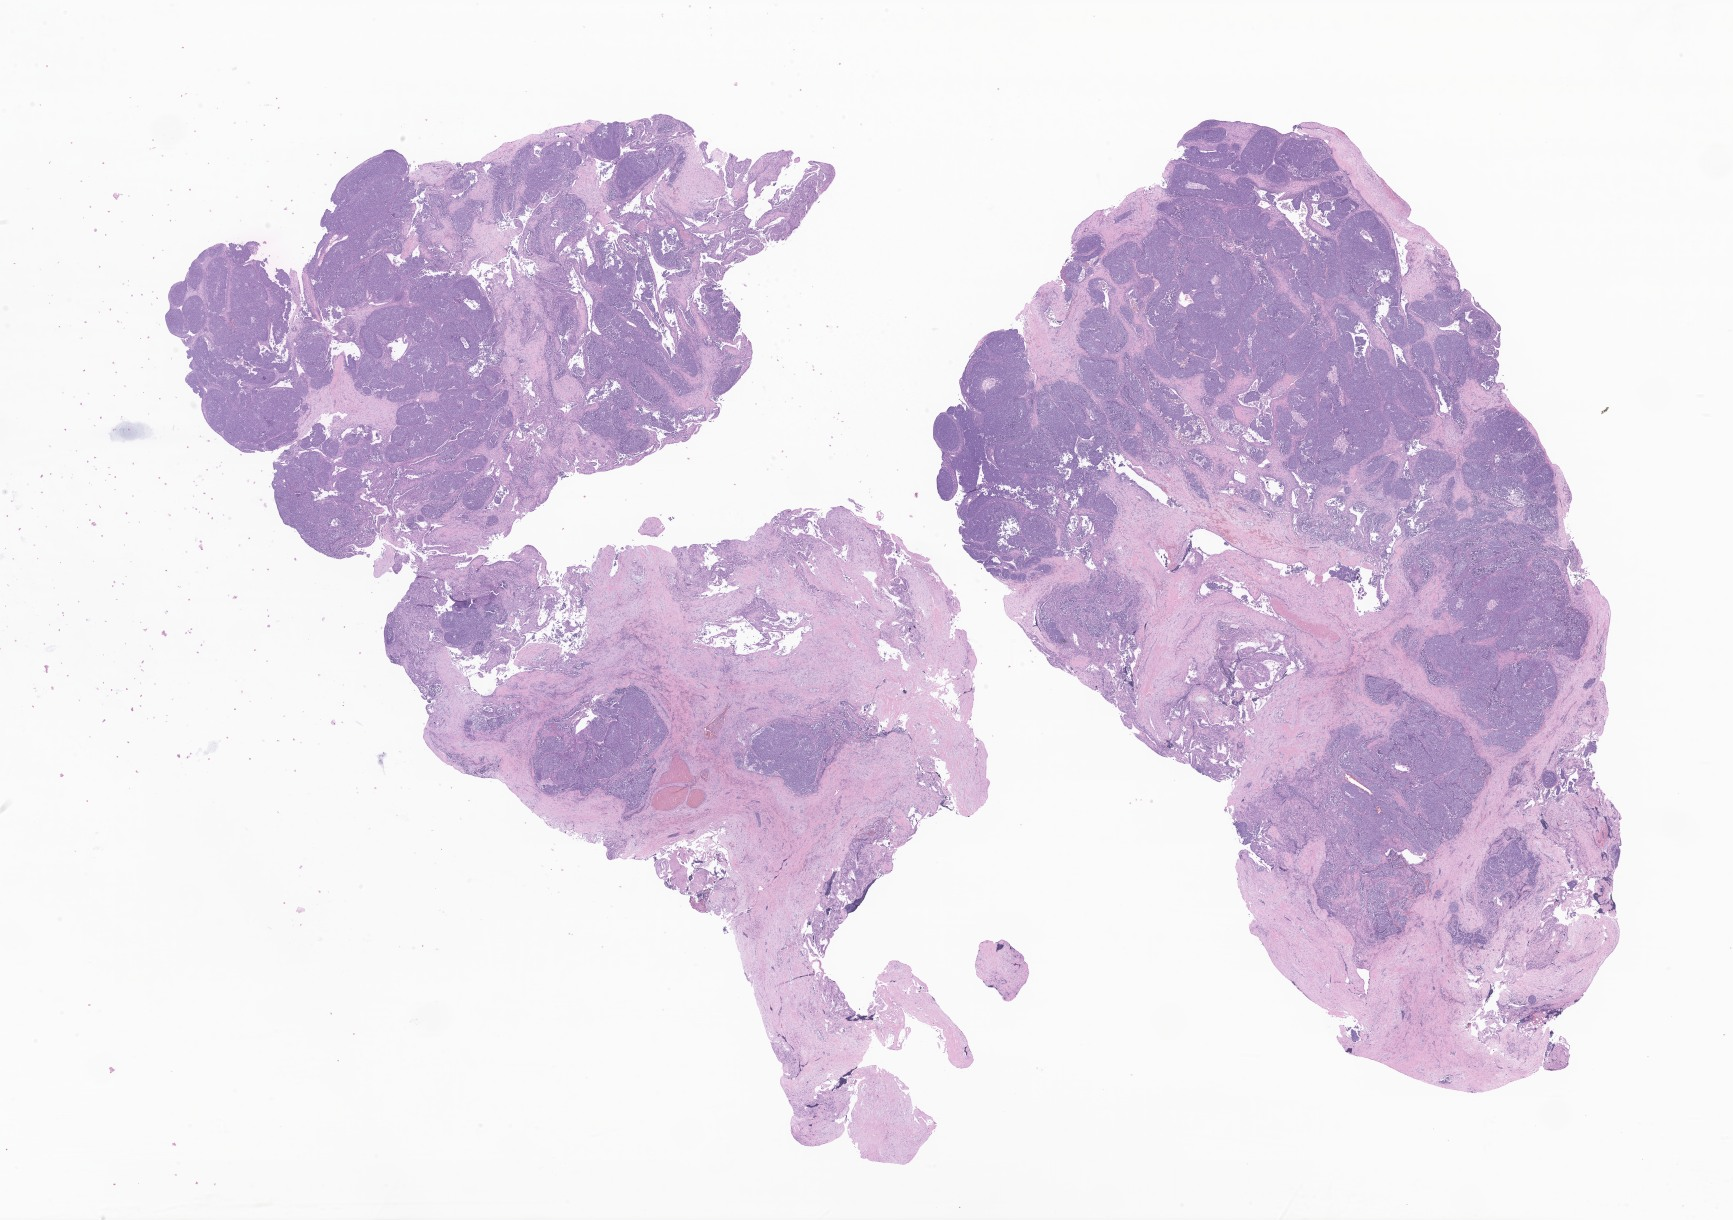
Hematoxylin and eosin (H&E) whole-slide image of tumor tissue from the mouth and/or pharynx, whole scanned area (about 29.2 x 20.6 mm) shown as a low-resolution overview. Formalin-fixed, paraffin-embedded (FFPE) tissue. Patient: female, age 726 days (about 2.0 years).
Tissue or organ of origin (case record): overlapping lesion of lip, oral cavity and pharynx. Diagnosis (ICD-O-3 morphology term): Mucoepidermoid carcinoma.